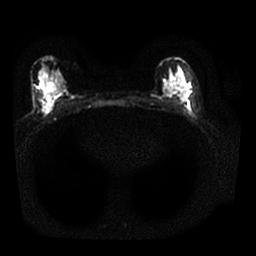
Breast MRI, one axial slice; slice 13 of 25 in the series (ordered by position); diffusion-weighted series; image 2 of 4 stored at this slice position (different b-values; order by instance number); 1.5 T; 4 mm slice thickness; 256 × 256 image matrix. Female patient.
Outlined on this slice (outlined manually by an expert reader):
- tumour on diffusion-weighted imaging: bounding box [x1, y1, x2, y2] px = [186, 91, 190, 97]